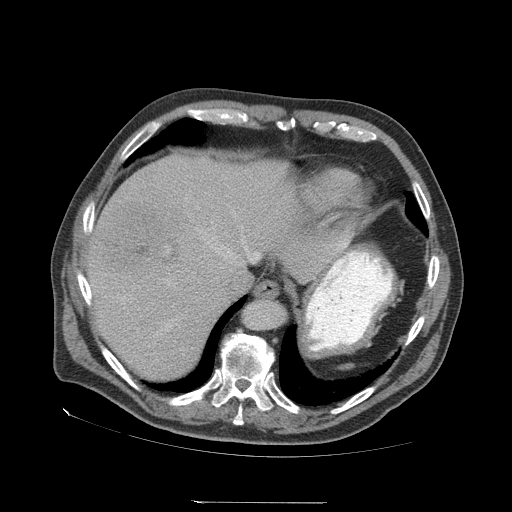
Contrast-enhanced abdominal CT (liver protocol), one axial slice; slice 55 of 83 in the series (ordered by position); 140 kVp; soft-tissue window (W 400 / L 40 HU); 2.5 mm slice thickness; 512 × 512 image matrix, field of view 460 × 460 mm. Case-level facts recorded for this patient, not image findings: diagnosis: hepatocellular carcinoma (patient treated with transarterial chemoembolisation; whether this scan precedes or follows treatment is not stated here); TNM stage (as recorded): Stage-I; Child-Pugh class: A; tumour differentiation: well differentiated; tumour nodularity: uninodular.
Structures marked on this image (semi-automatic segmentation, software-assisted and operator-edited):
- liver parenchyma outside the tumour (the mass and vessels are separate outlines, so this box may not span the whole liver): box from (x=84, y=154) to (x=300, y=378) px
- mass: (x=89, y=203)–(x=177, y=287)
- liver vessels: (x=169, y=240)–(x=259, y=328)